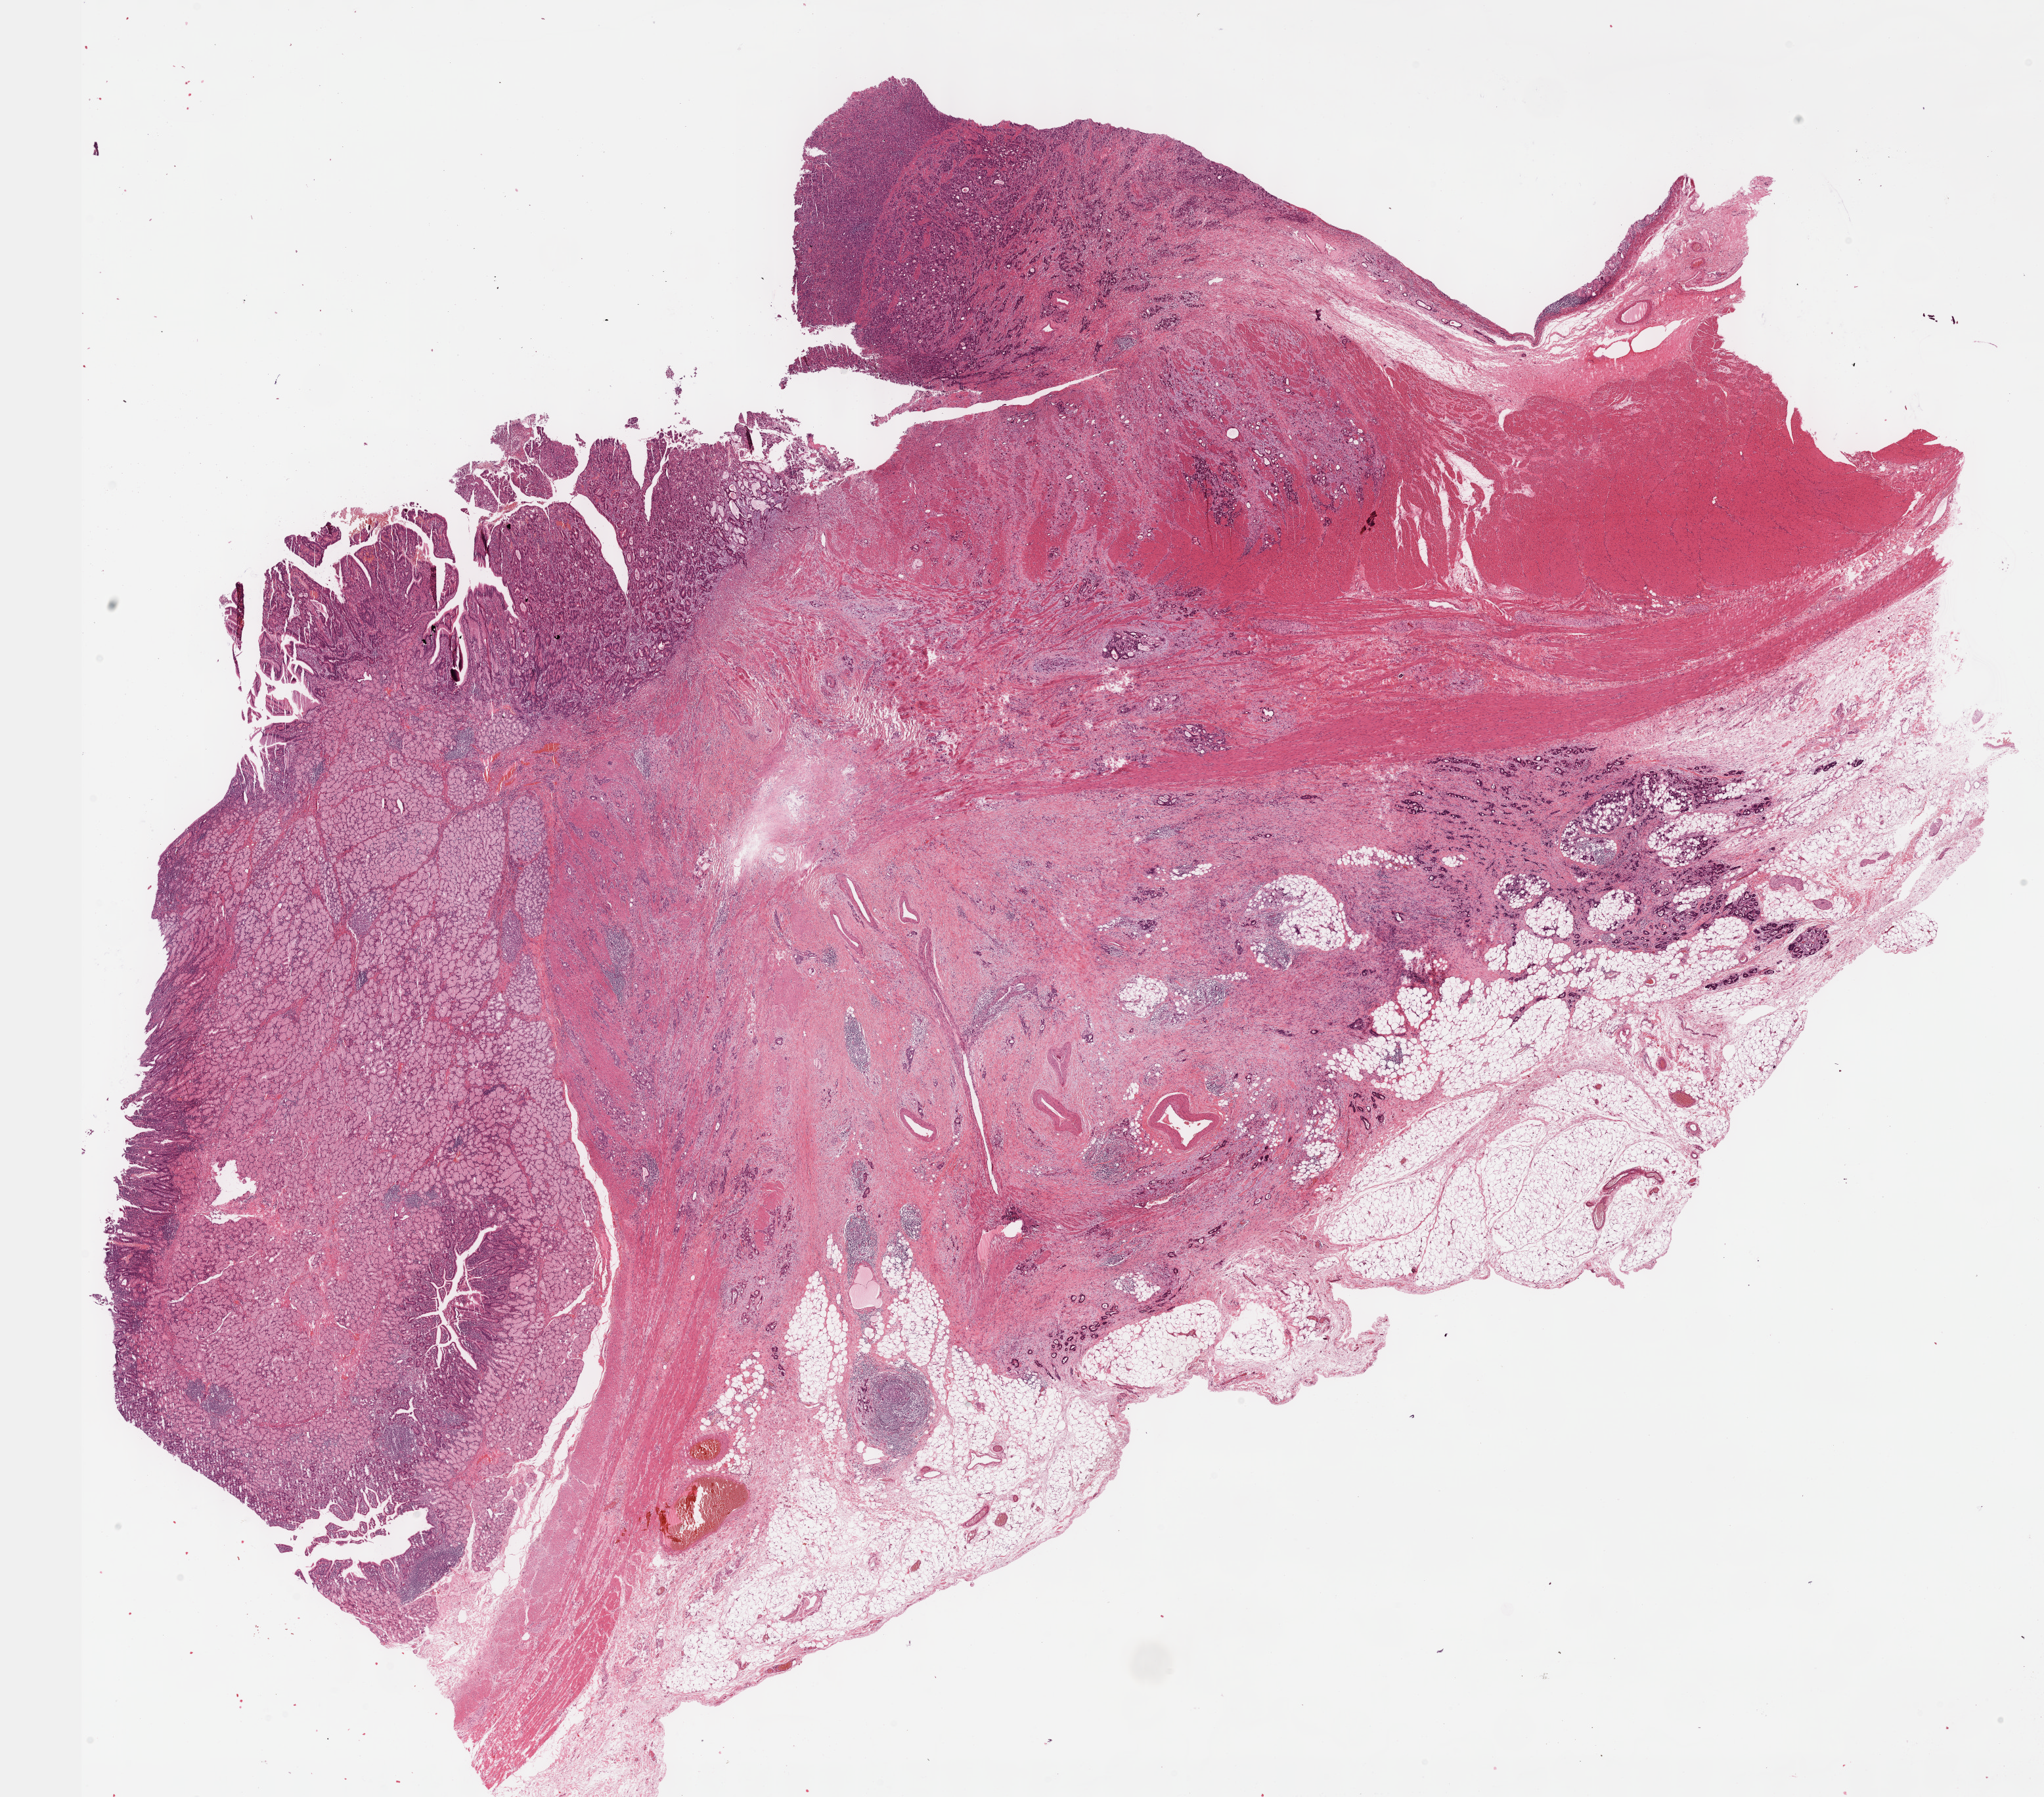
Digitized H&E-stained tissue section (whole slide), shown as a low-resolution overview of the whole scanned area (about 25.1 x 22.1 mm, acquisition: 40x scan). Formalin-fixed paraffin-embedded (FFPE) diagnostic section. Stomach, primary tumour sample. Female patient; age at initial diagnosis 47 years.
Diagnosis: Tubular adenocarcinoma (gastric antrum).